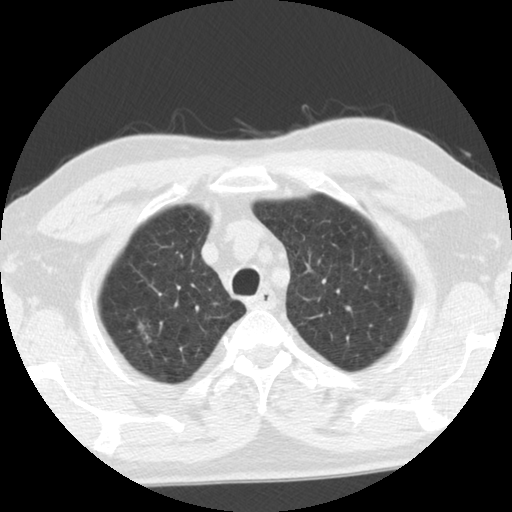
Low-dose screening chest CT, one axial slice; position 95 of 116 along the scan axis; reconstruction kernel STANDARD; 140 kVp; lung window (W 1500 / L -600 HU); 2.5 mm slice thickness; 512 × 512 image matrix.
Structures marked on this image (expert manual segmentation):
- lesion 1 (tumor, upper lobe of right lung): bounding box <137,318,157,346> (left, top, right, bottom; pixels)